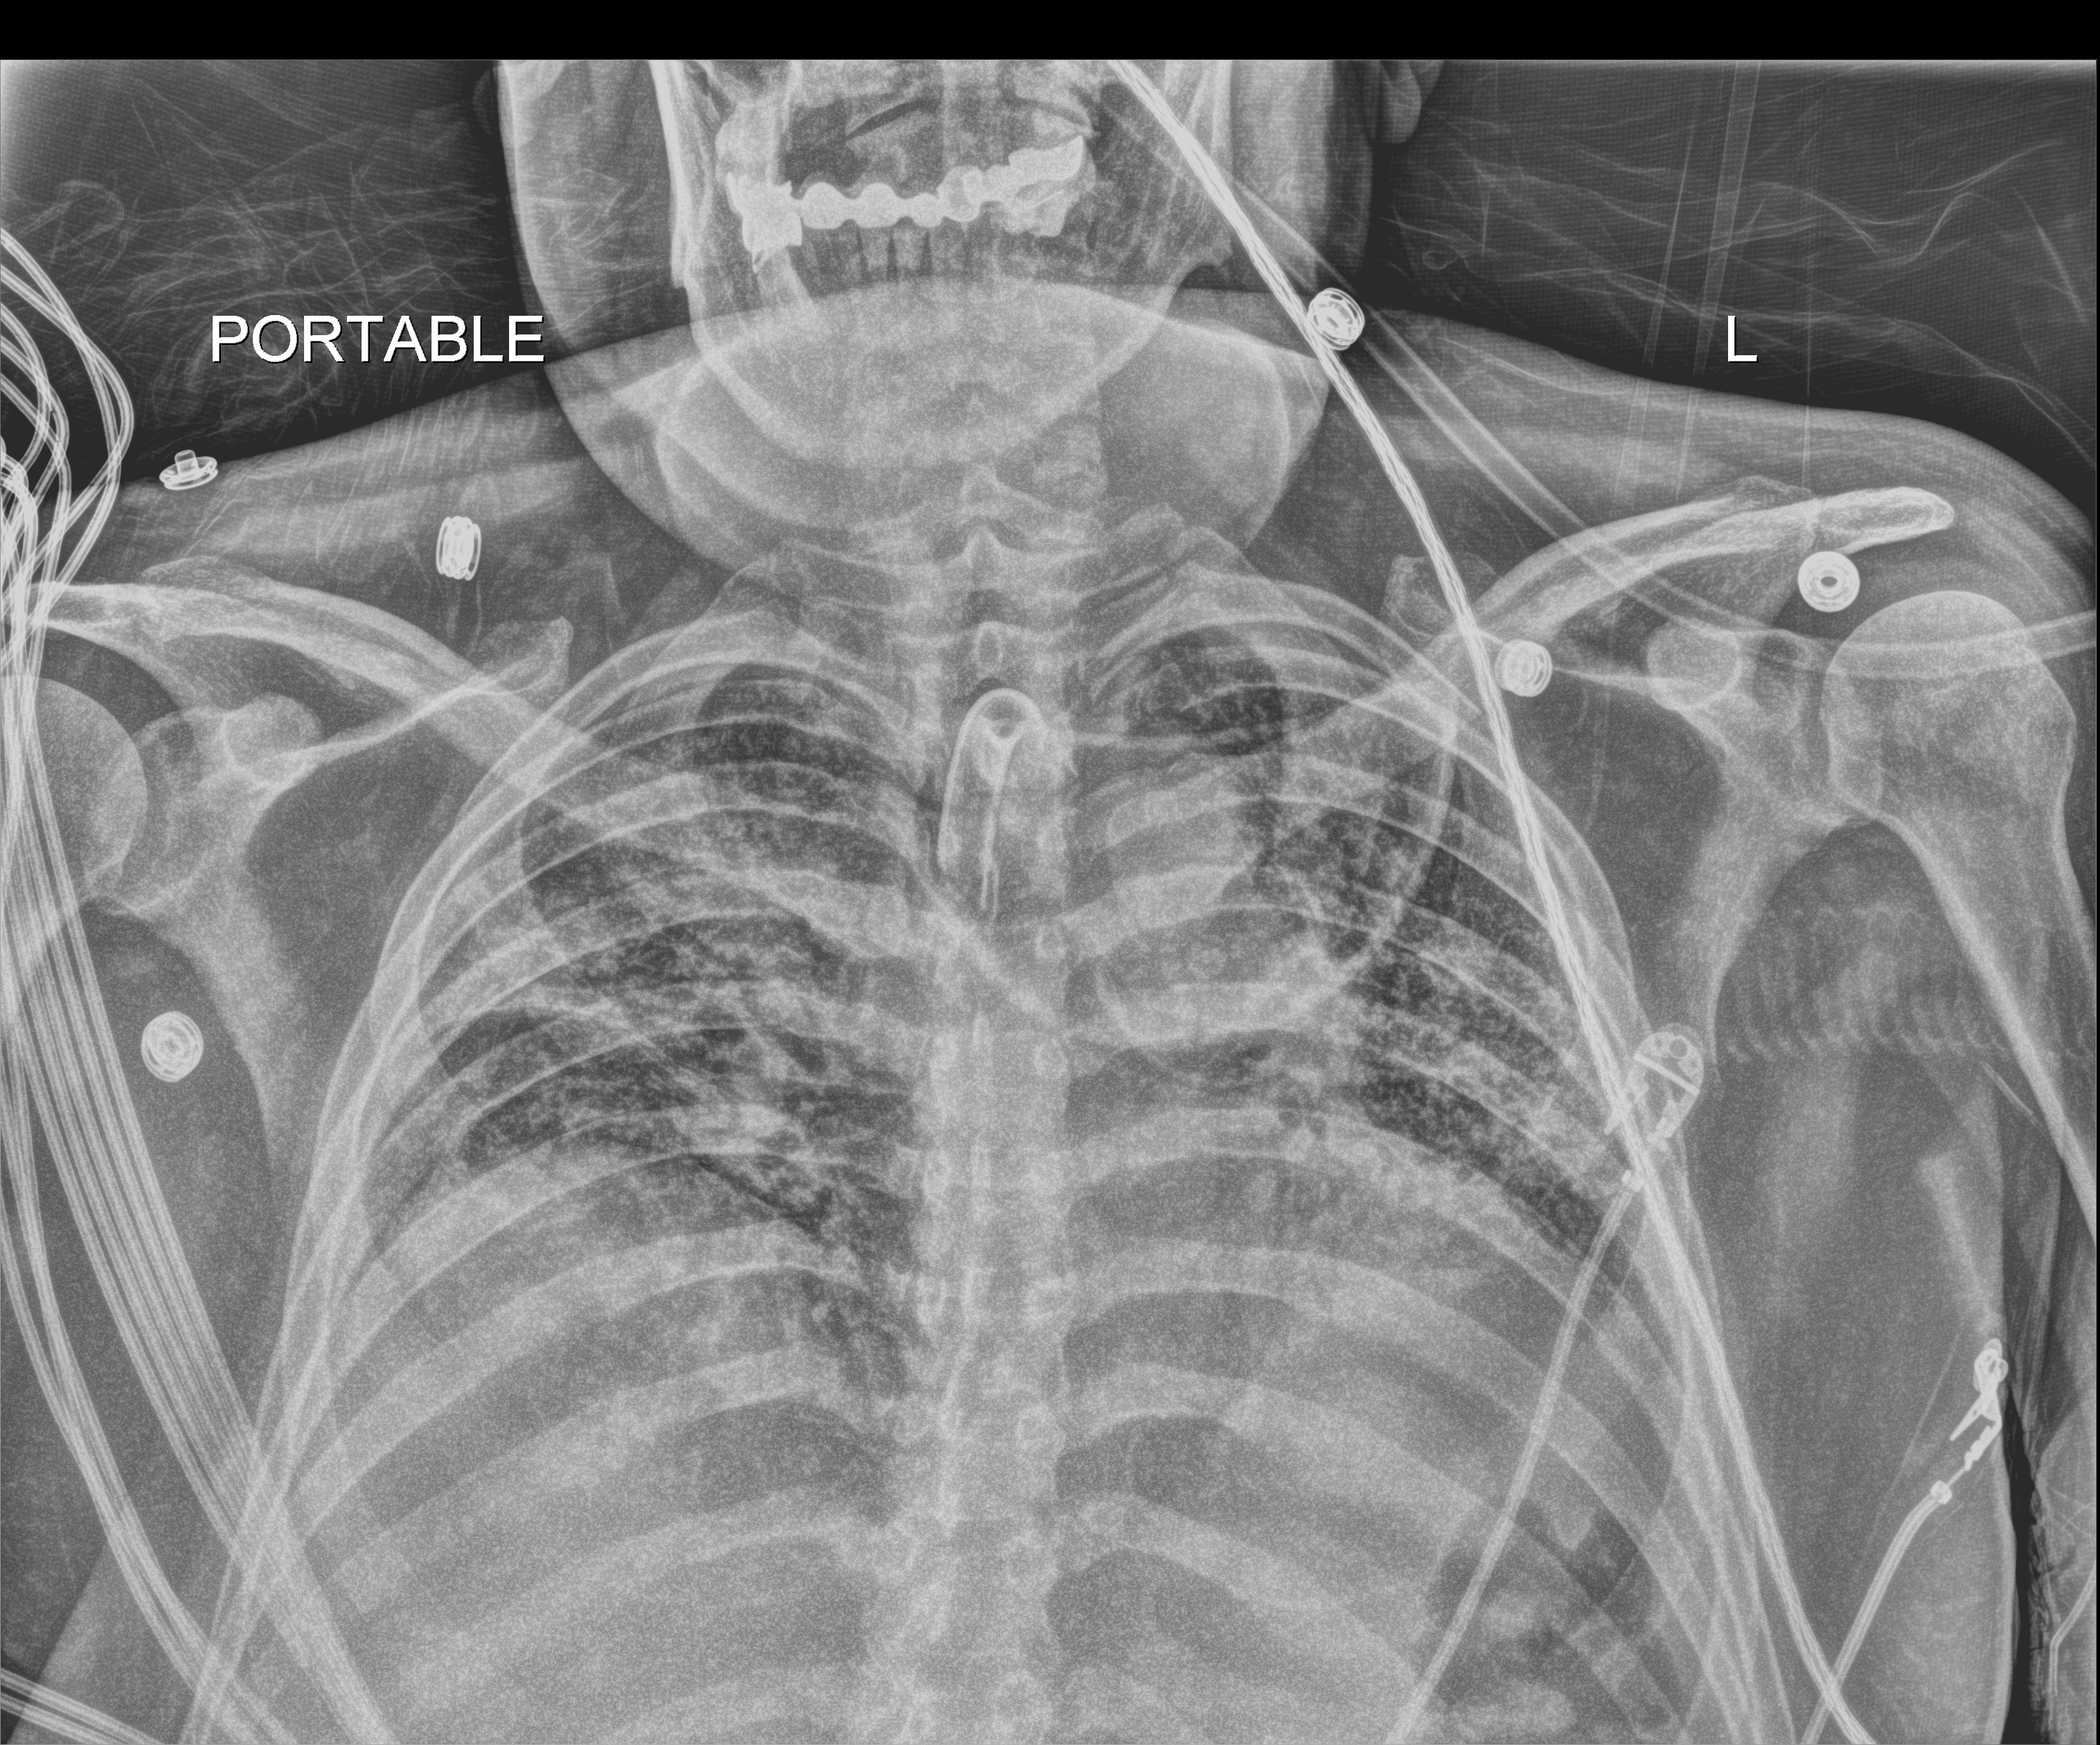
Bedside chest radiograph (digital radiography). Patient hospitalised with COVID-19; male, aged 18–59 years.
From the hospital-stay record, not from the radiograph (when in the stay this image was taken is not recorded):
- length of hospital stay: 96 days